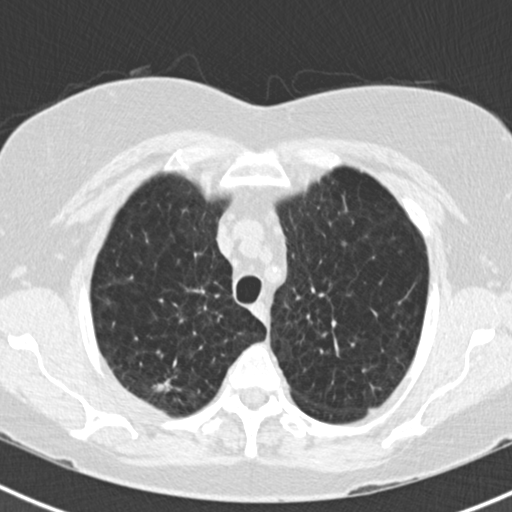
Low-dose screening chest CT, one axial slice. Position 140 of 180 along the scan axis. Reconstruction kernel B30f. 120 kVp. Lung window (W 1500 / L -600 HU). 2 mm slice thickness. 512 × 512 image matrix, field of view 310 × 310 mm.
Structures marked on this image (outlined manually by an expert reader):
- lesion 1 (tumor, upper lobe of right lung): bounding box (x1, y1, x2, y2) in pixels: (154, 379, 172, 392)